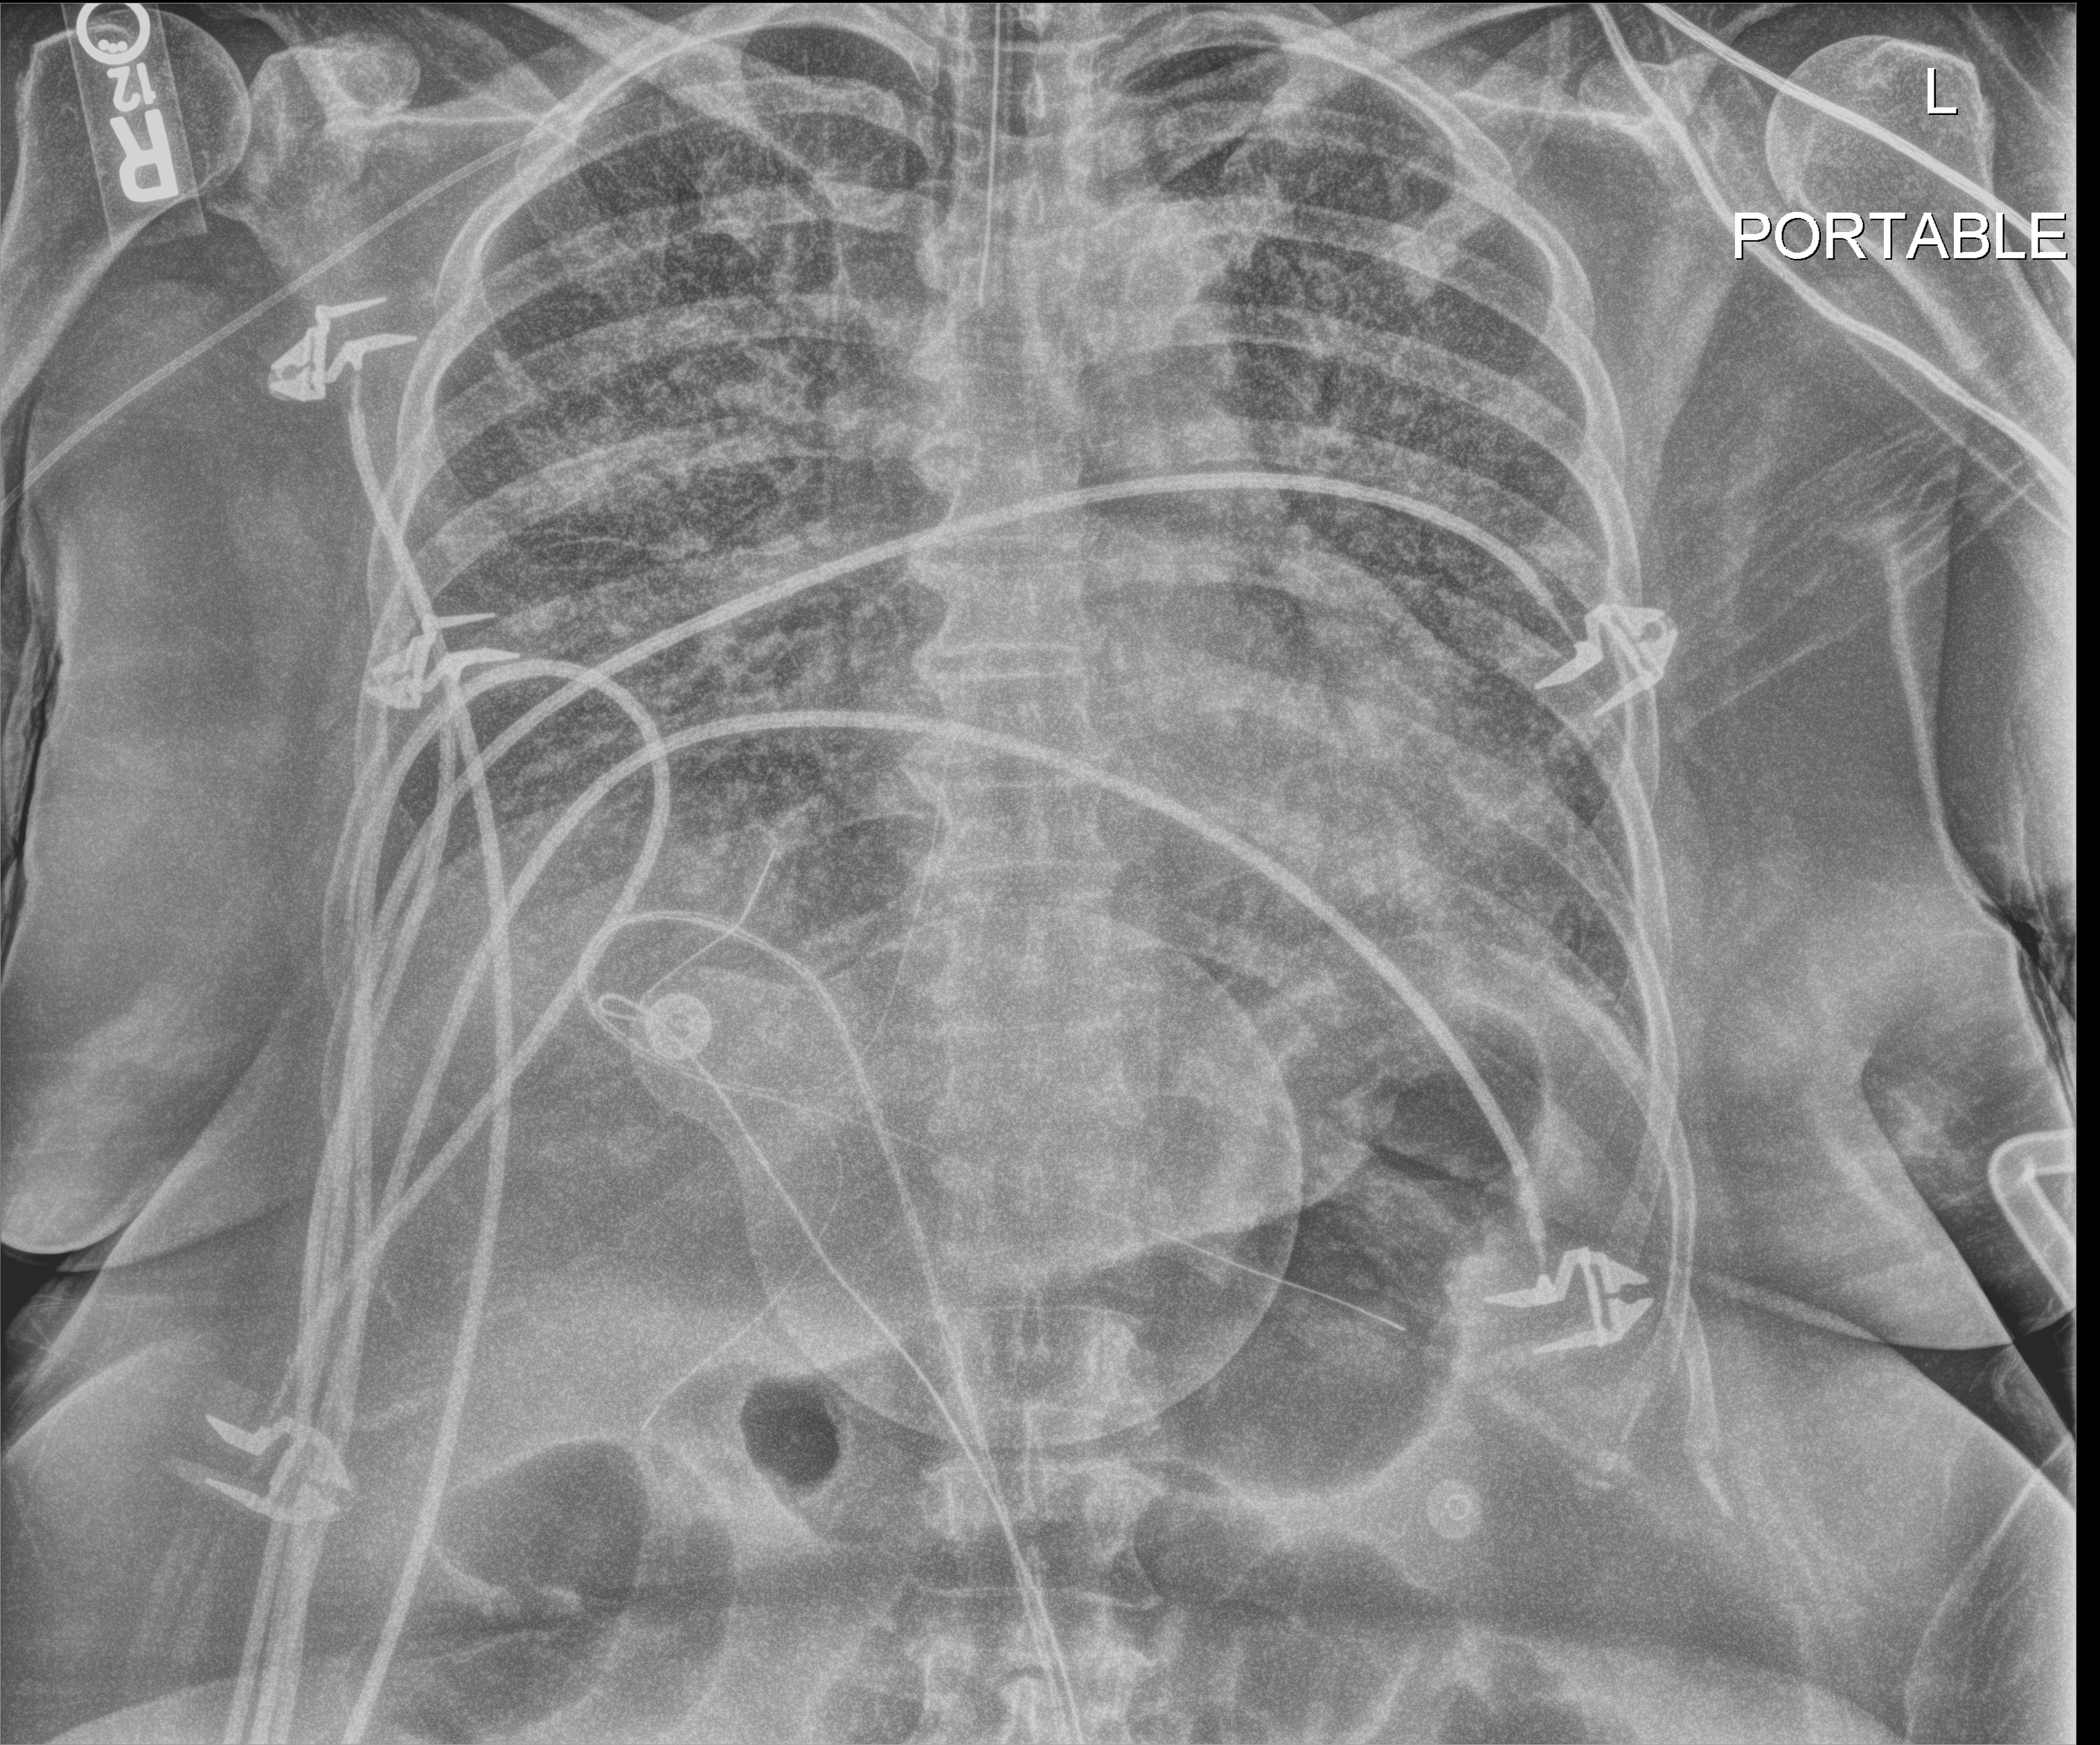
Chest X-ray (portable). Female patient hospitalised with COVID-19, age 60–74 years.
Hospital-stay facts (about this admission, not read from this image; timing relative to this image not recorded):
- admitted to intensive care during this hospital stay: yes